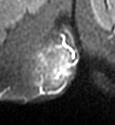
MRI of an extremity soft-tissue mass, one axial slice. Slice 12 of 49 in the series (ordered by position). STIR. MR volume resampled by the dataset authors to the PET/CT grid (not the native acquisition matrix). 3.27 mm slice thickness. 115 × 125 image matrix, field of view 112 × 122 mm. Female patient. Case-level facts recorded for this patient, not image findings: histological type: epithelioid sarcoma; grade: intermediate; site of the primary tumour: right buttock.
Annotated regions visible in this slice (expert contour drawn on MRI and transferred to this co-registered scan by the dataset authors):
- gross tumour volume including surrounding oedema: bounding box [x1, y1, x2, y2] px = [33, 44, 71, 90]